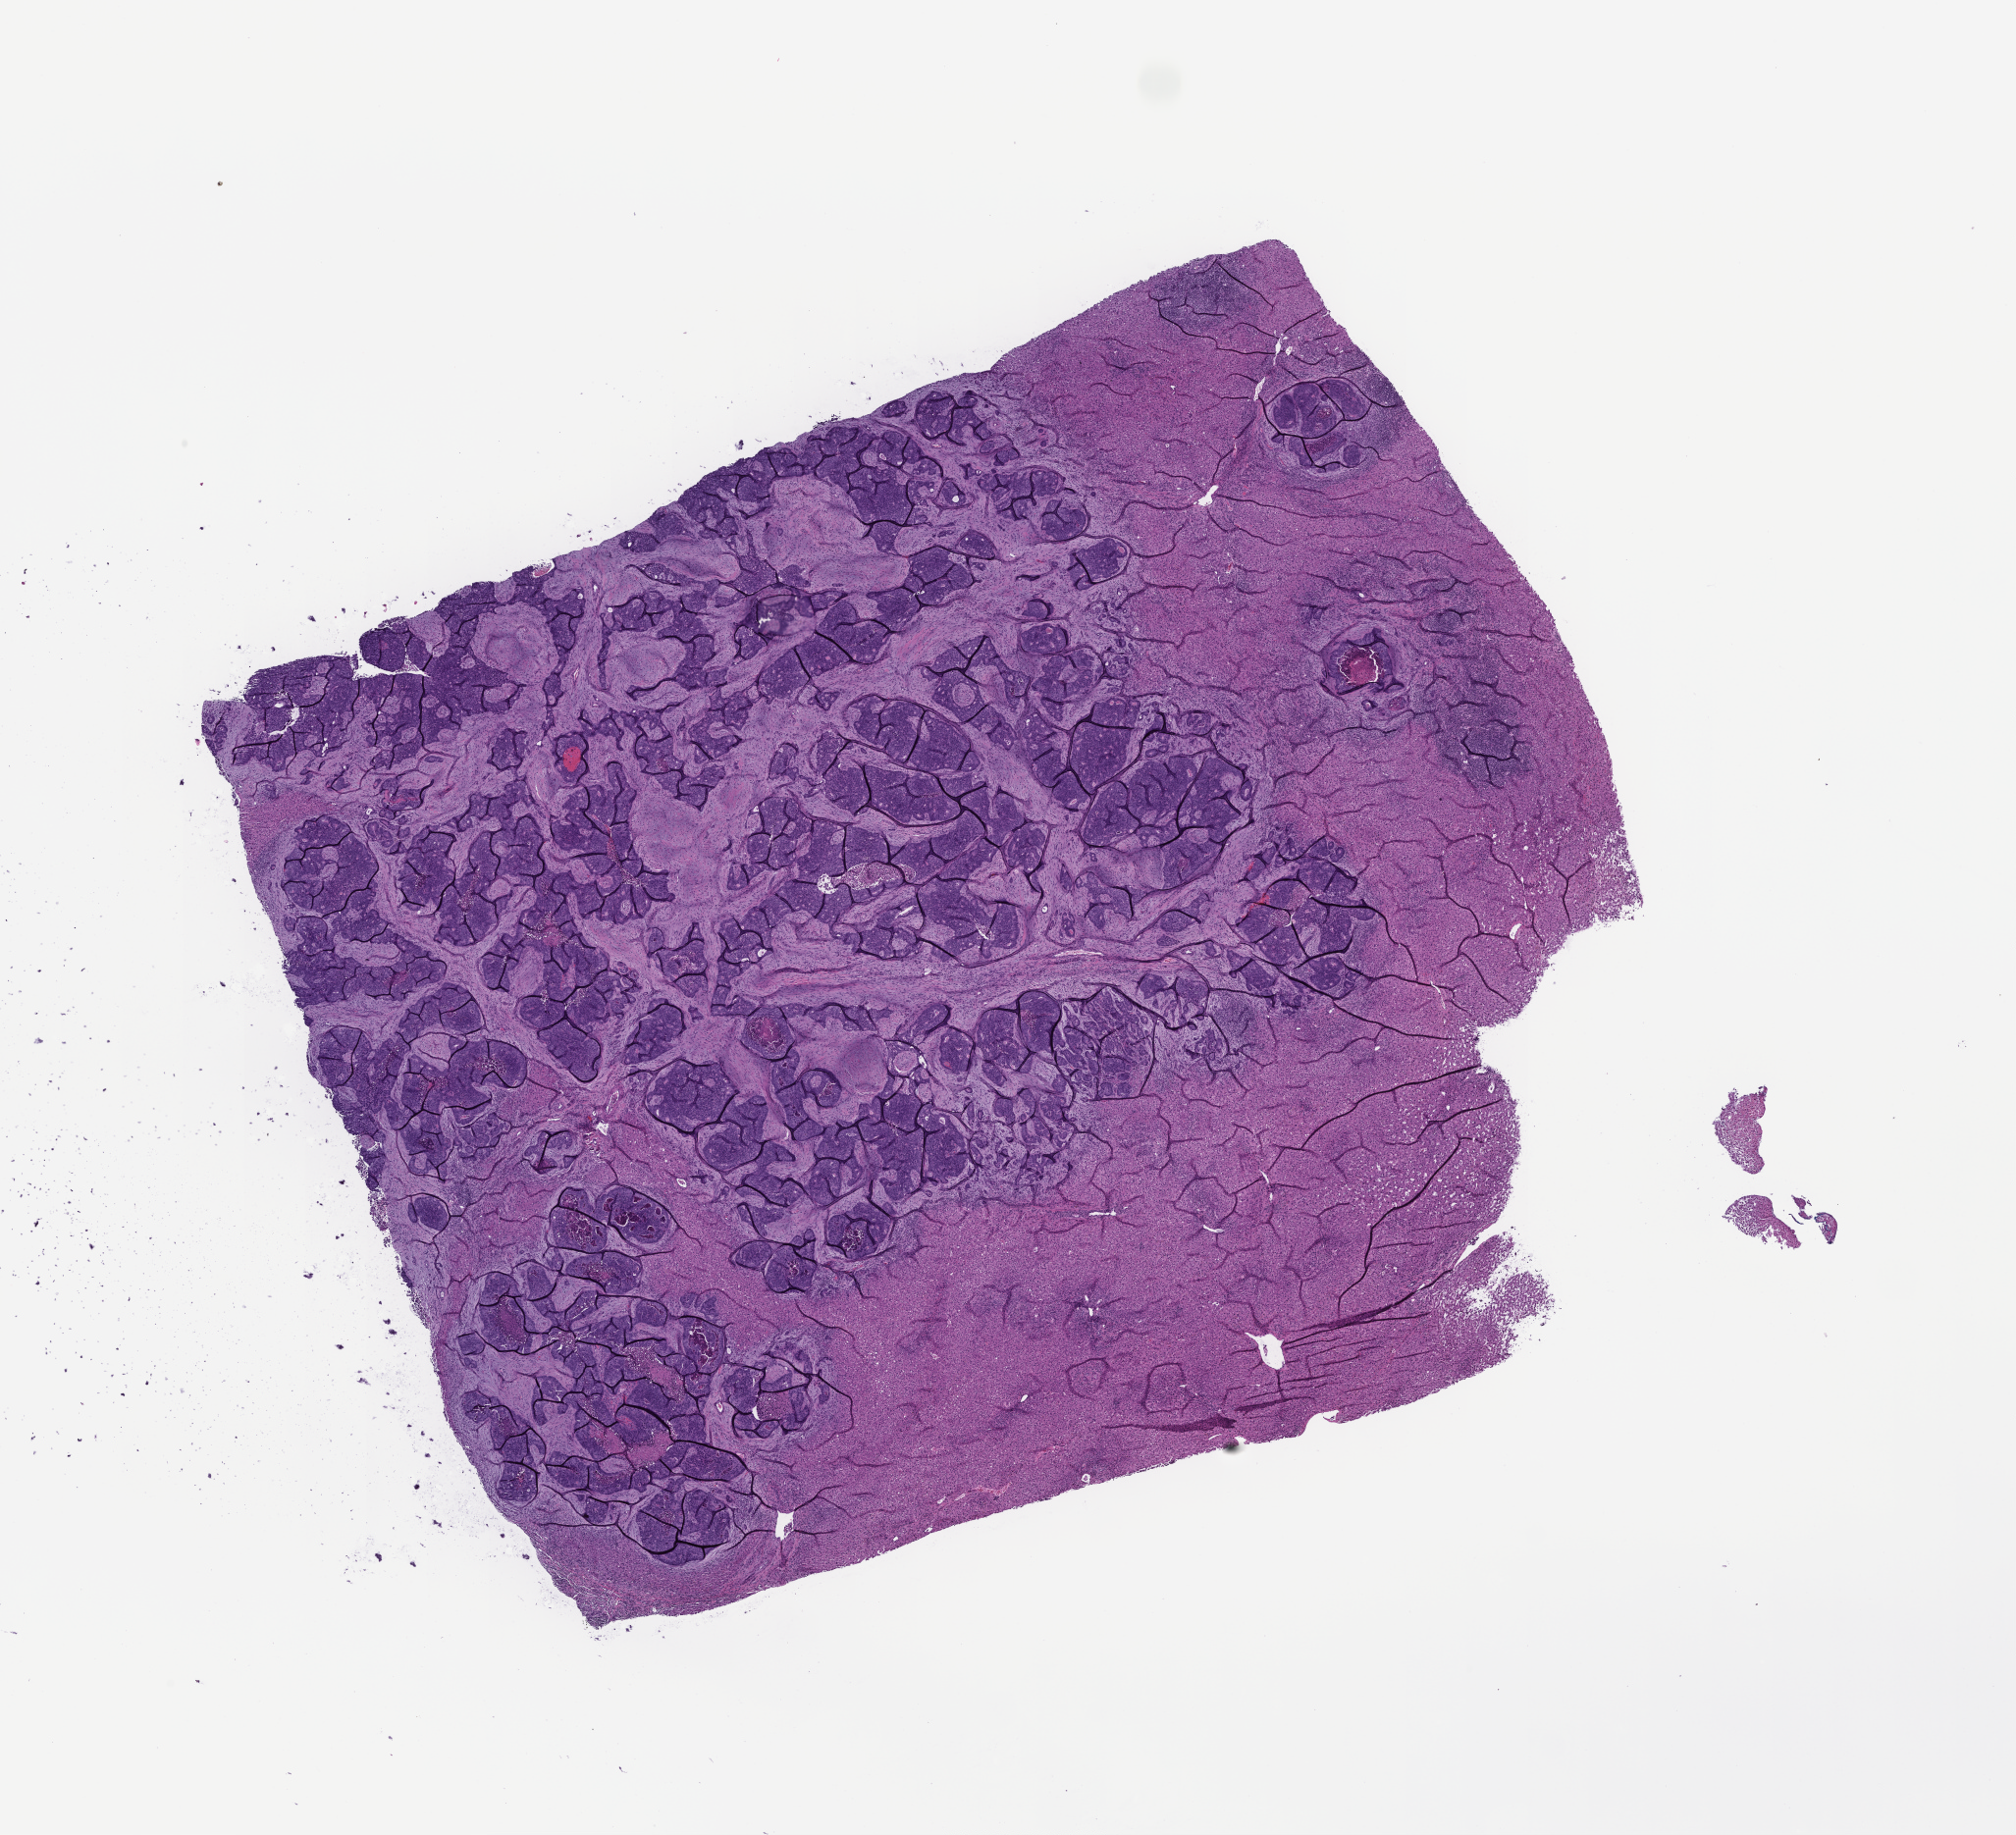
Whole-slide image, H&E stain, whole scanned area (about 16.6 x 15.1 mm) shown as a low-resolution overview; formalin-fixed, paraffin-embedded (FFPE) tissue; specimen time point: collected on treatment. Patient sex: female.
• this section: metastatic tumor tissue
• patient diagnosis (primary): Colorectal Carcinoma